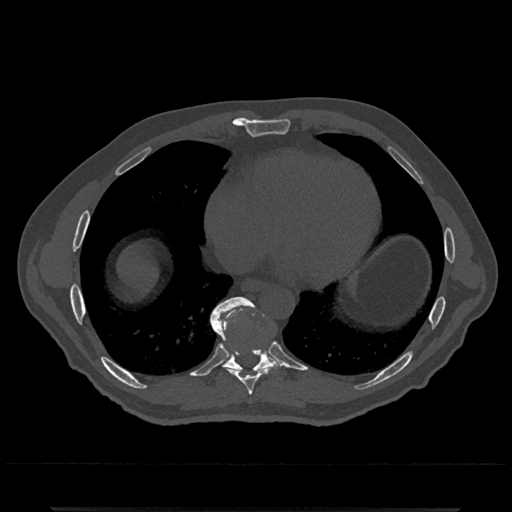
CT including the spine, one axial slice. Slice 643 of 797 in the series (ordered by position). Reconstruction kernel Br40s/3. Bone window (W 1800 / L 400 HU). 512 × 512 image matrix, field of view 393 × 393 mm. Patient: male, 67 years. From the clinical record (not read from this slice): primary cancer: prostate.
Structures marked on this image (semi-automatic segmentation, software-assisted and operator-edited):
- T8 vertebra: bounding box (x1, y1, x2, y2) in pixels: (212, 325, 278, 395)
- T9 vertebra: (210, 297, 280, 373)